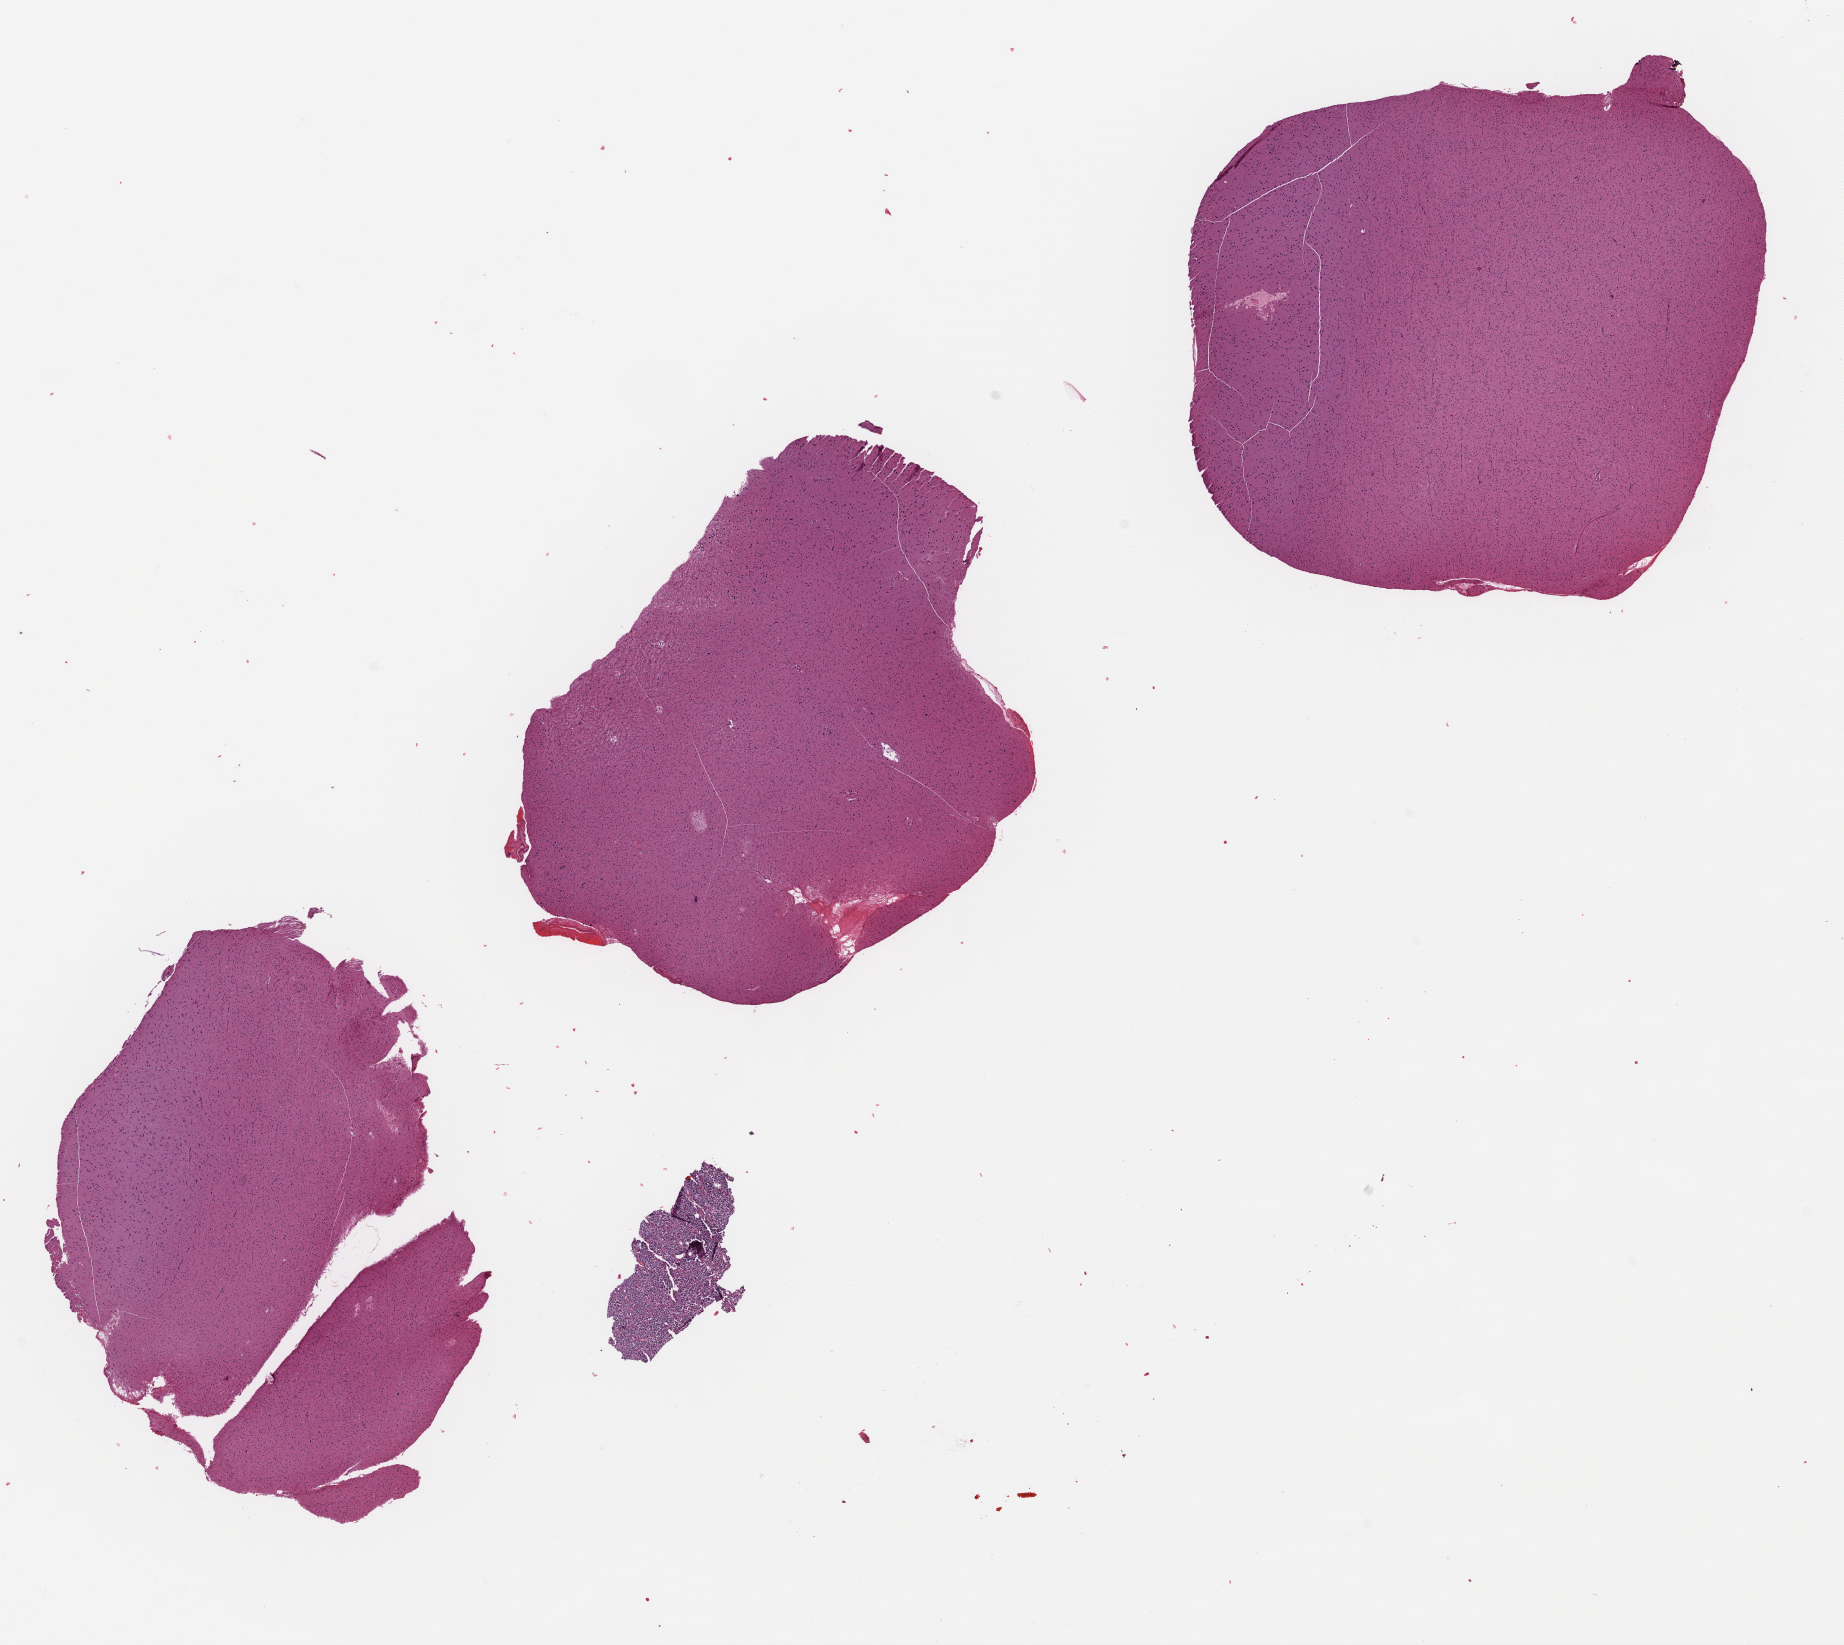
Whole-slide histology image, Hematoxylin and eosin (H&E) stained — shown as a low-resolution overview of the whole scanned area (about 14.5 x 12.9 mm, slide scanned at 40x); formalin-fixed paraffin-embedded (FFPE) diagnostic section; primary tumour sample from the brain. Female, age 61 years at initial diagnosis. Histologic grade: G2 (moderately differentiated).
* histologic diagnosis: Astrocytoma, NOS